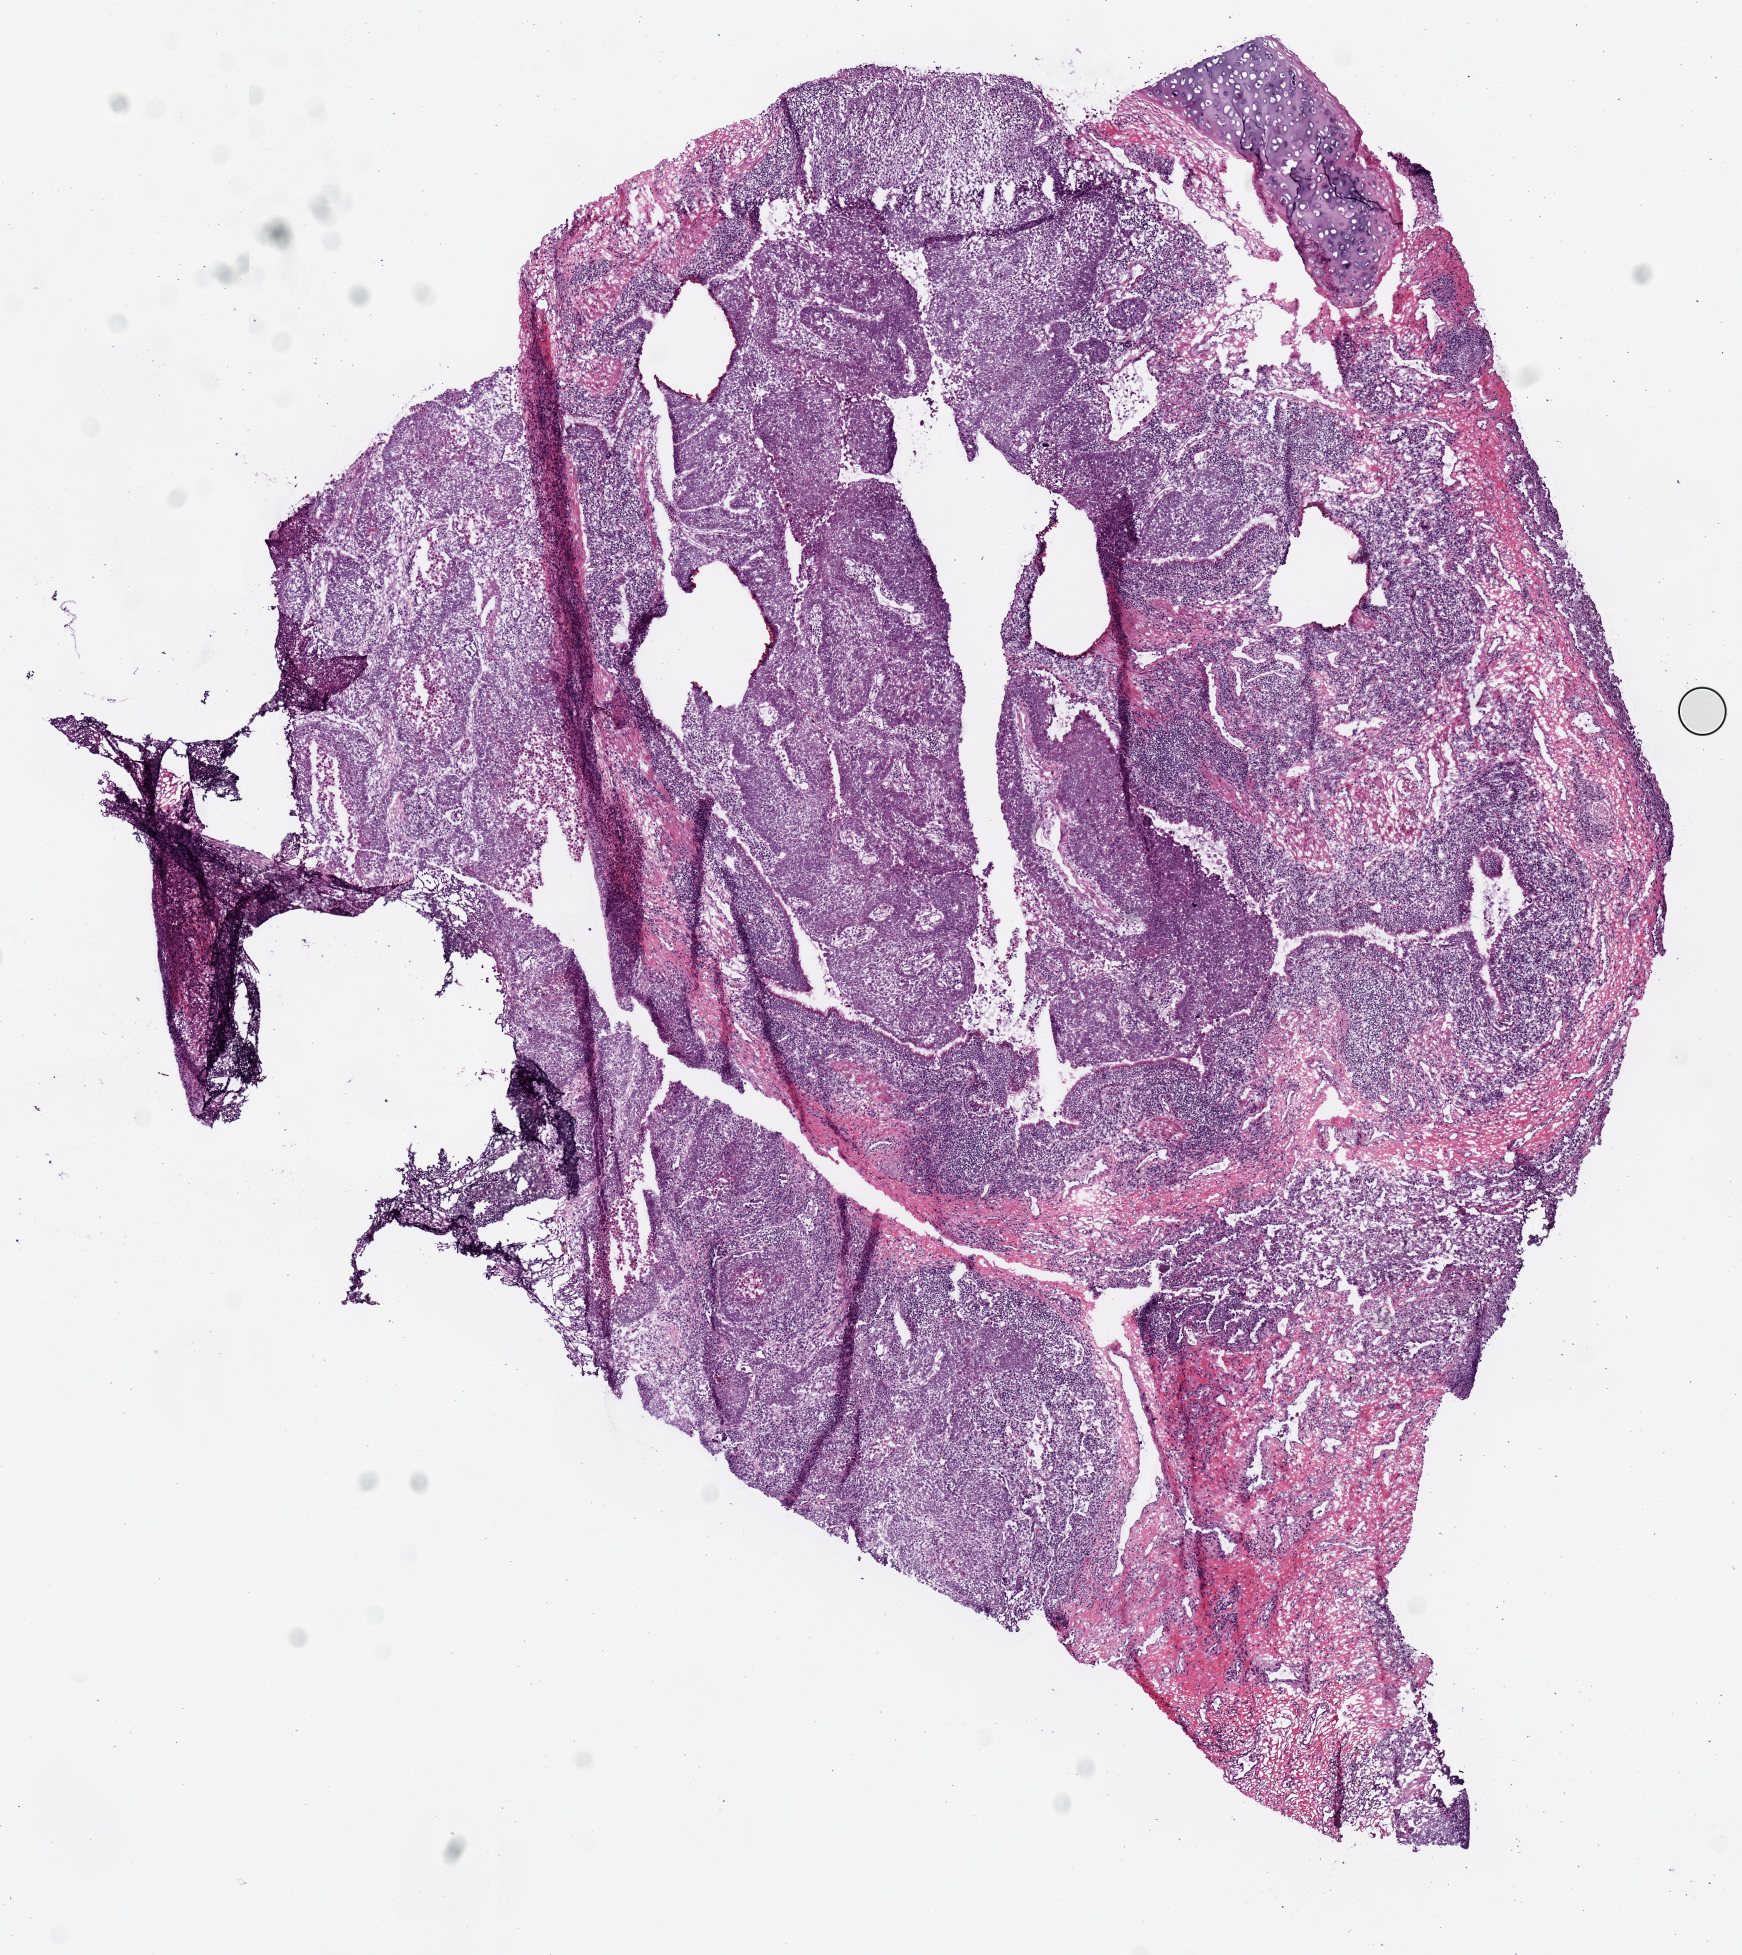
Digitized H&E tissue section (whole slide), low-resolution overview of the scanned area, about 6.9 x 7.7 mm. Frozen section from the top of the tissue portion. Primary tumour sample from the lung. Male, age 70 years at initial diagnosis. Composition of this section per pathologist review: tumour nuclei 75%, necrosis 0%.
• AJCC pathologic stage: IIB (7th edition)
• diagnosis: Squamous cell carcinoma, NOS
• laterality: right